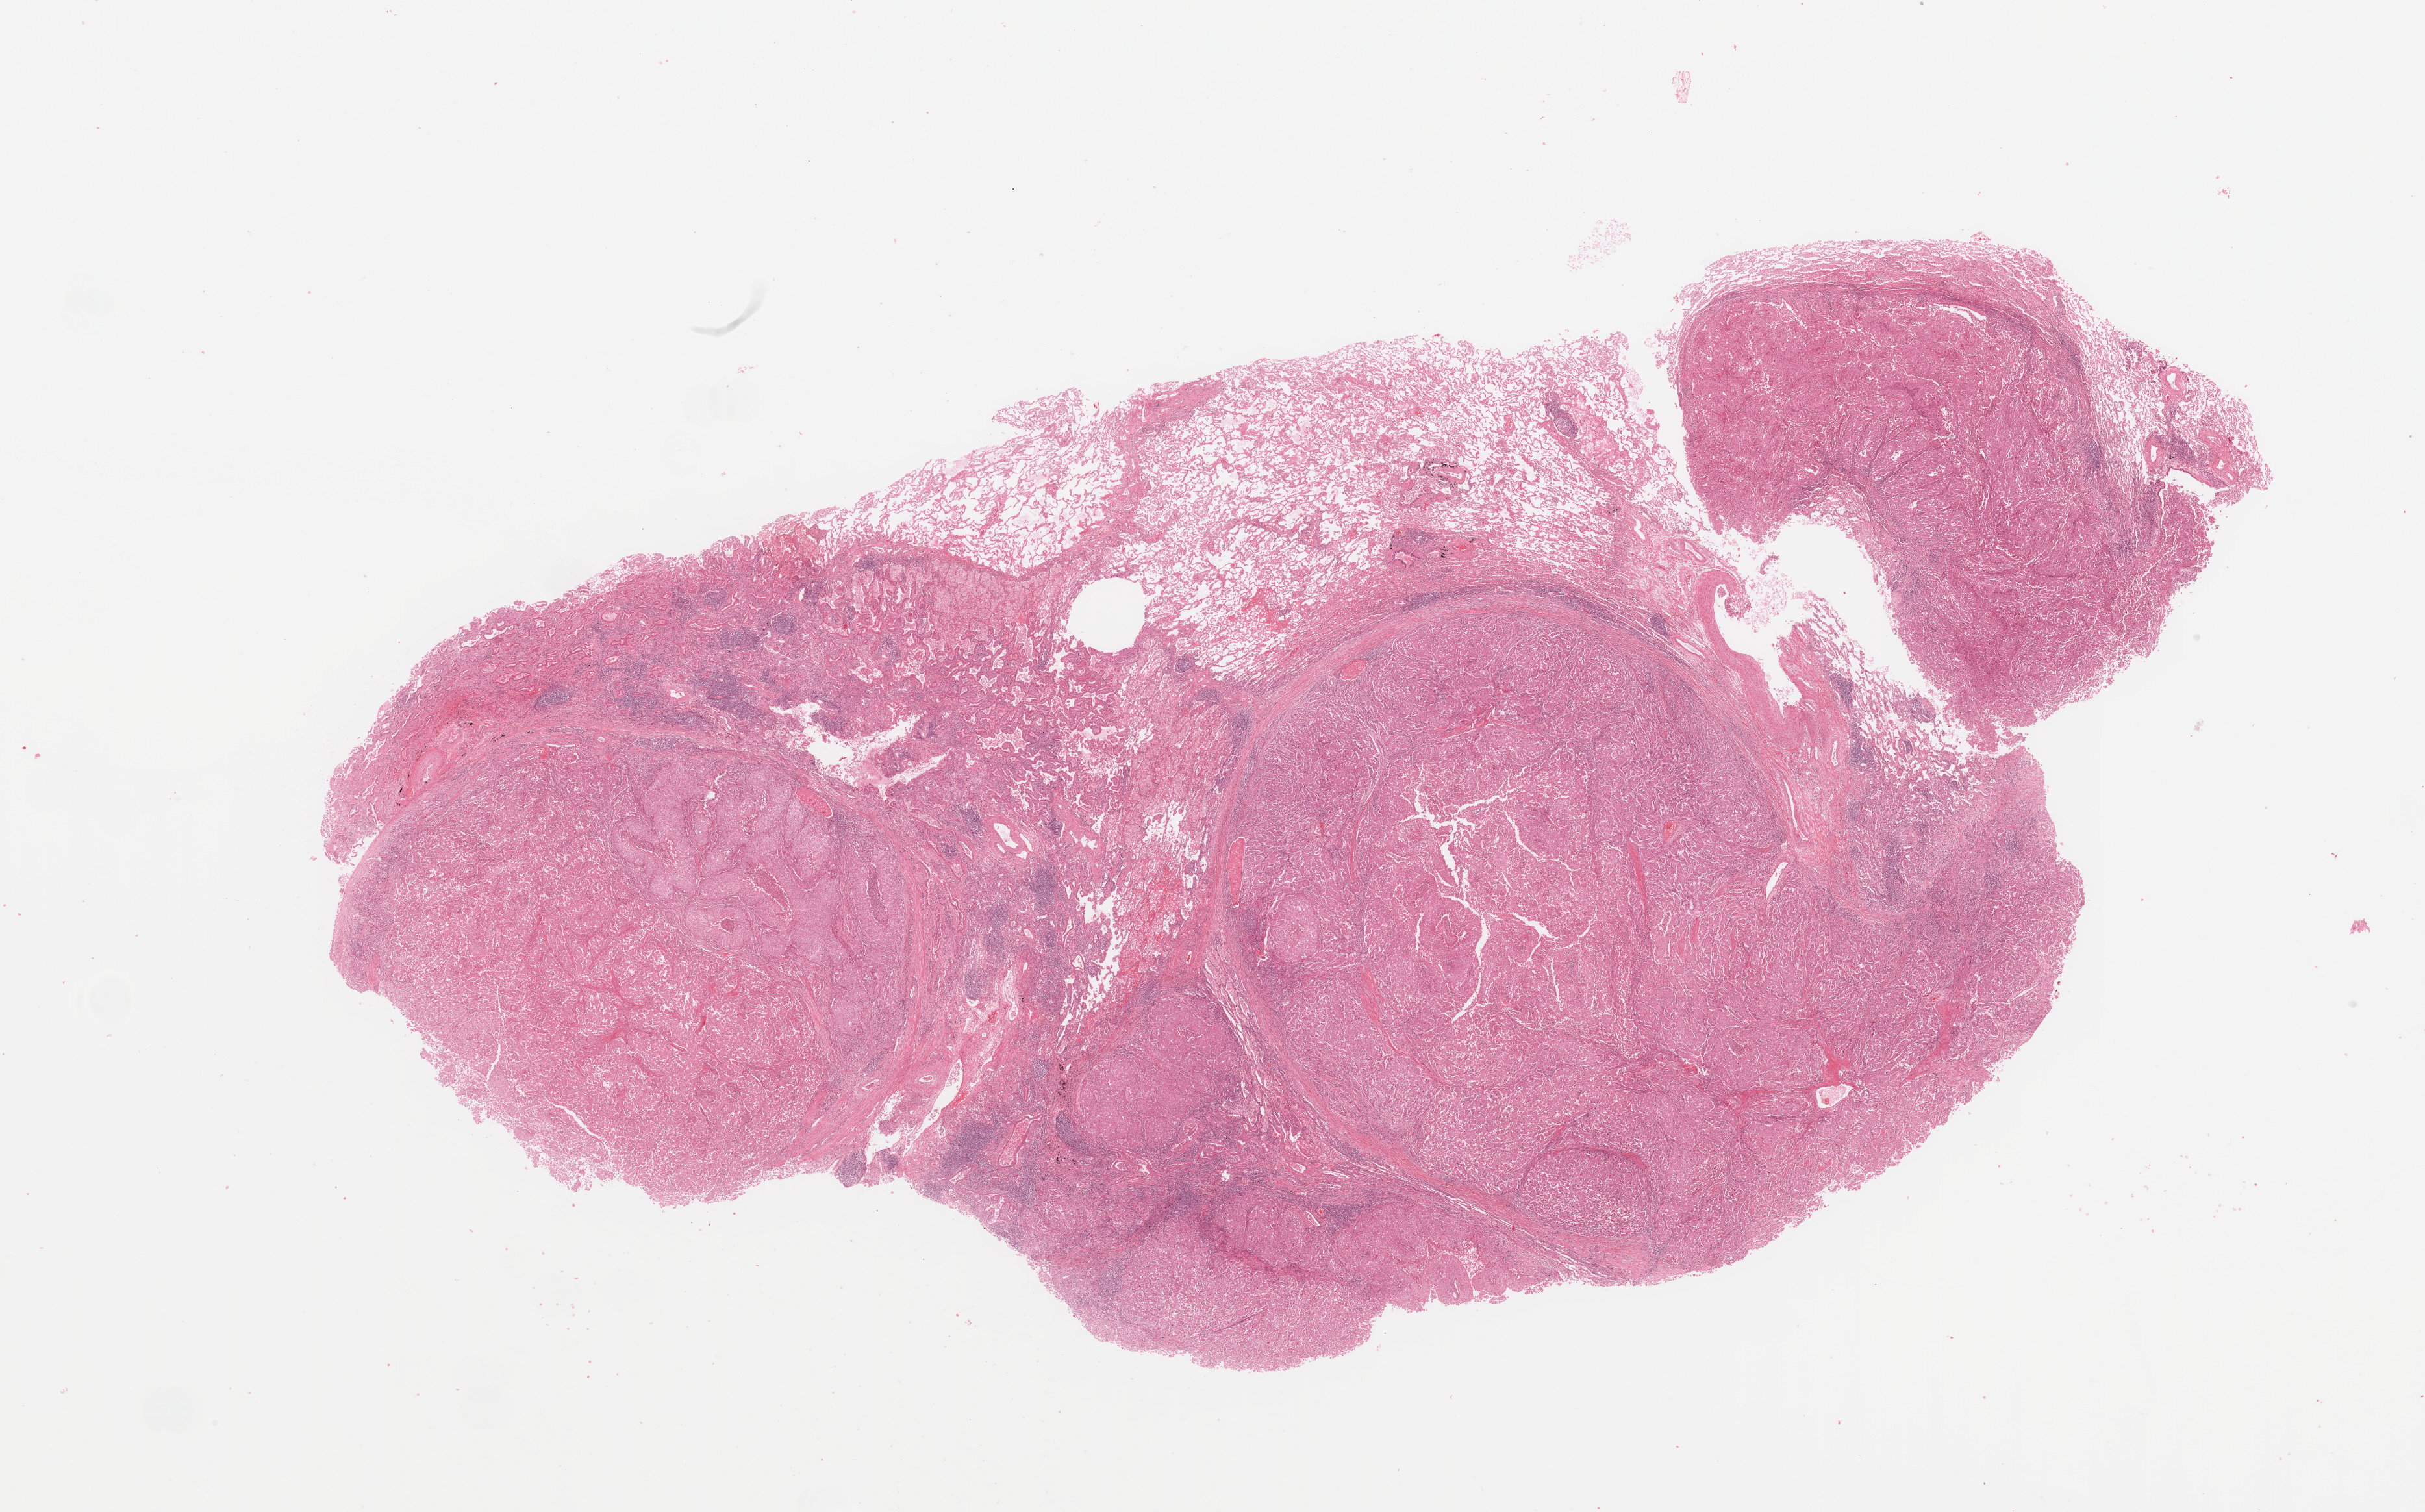
H&E-stained whole-slide image, whole scanned area (about 29.5 x 18.4 mm) shown as a low-resolution overview, tumour tissue sample, sampled site: lung. Female, 47 y/o. Histologic grade: G3 (poorly differentiated). Slide review estimates, as recorded: tumour nuclei 70%, necrosis 5%.
• histologic diagnosis: Adenocarcinoma, NOS
• AJCC pathologic stage: IIIA